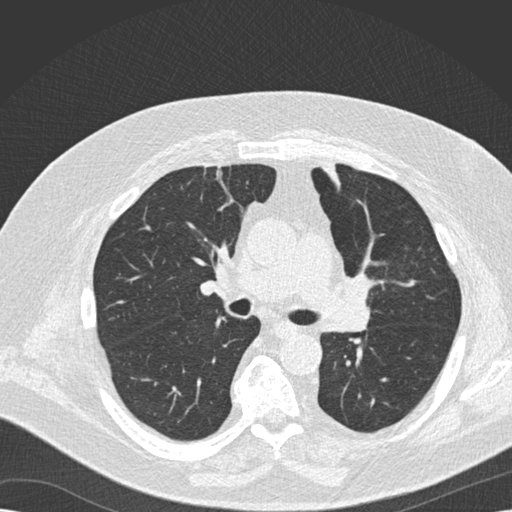
Low-dose screening chest CT, one axial slice. Reconstruction kernel B30f. Lung window (W 1500 / L -600 HU). 2 mm slice thickness. 512 × 512 image matrix, field of view 370 × 370 mm.
Structures marked on this image (expert manual segmentation):
- lesion 1 (tumor, upper lobe of left lung): bounding box (x1, y1, x2, y2) in pixels: (322, 159, 341, 181)